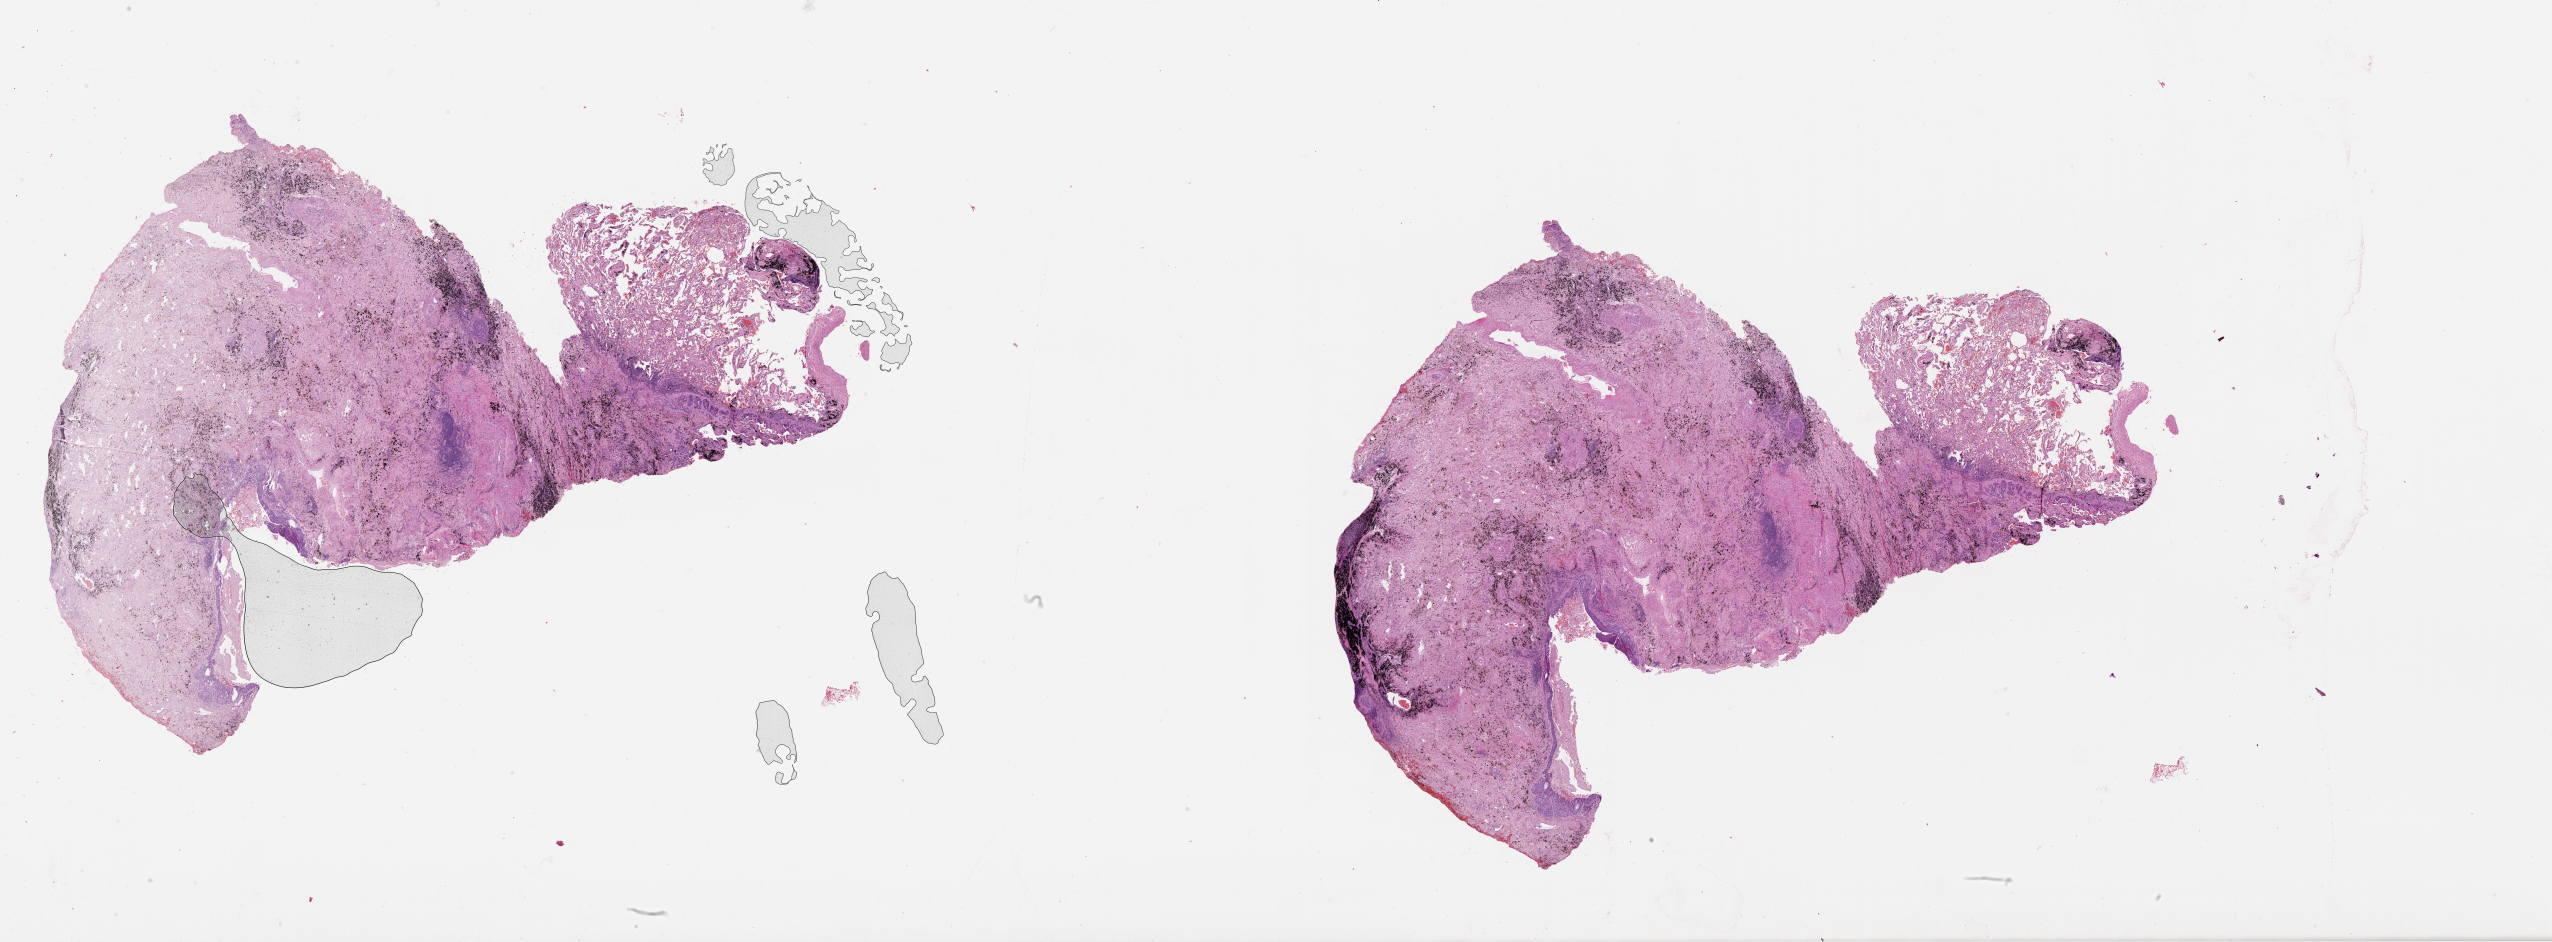
H&E whole-slide image, a low-resolution overview of the entire scanned area, about 41.1 x 15.2 mm (slide scanned at 20x); lung, tissue type not recorded.
Patient diagnosis (cohort enrolment): squamous cell carcinoma (lung).